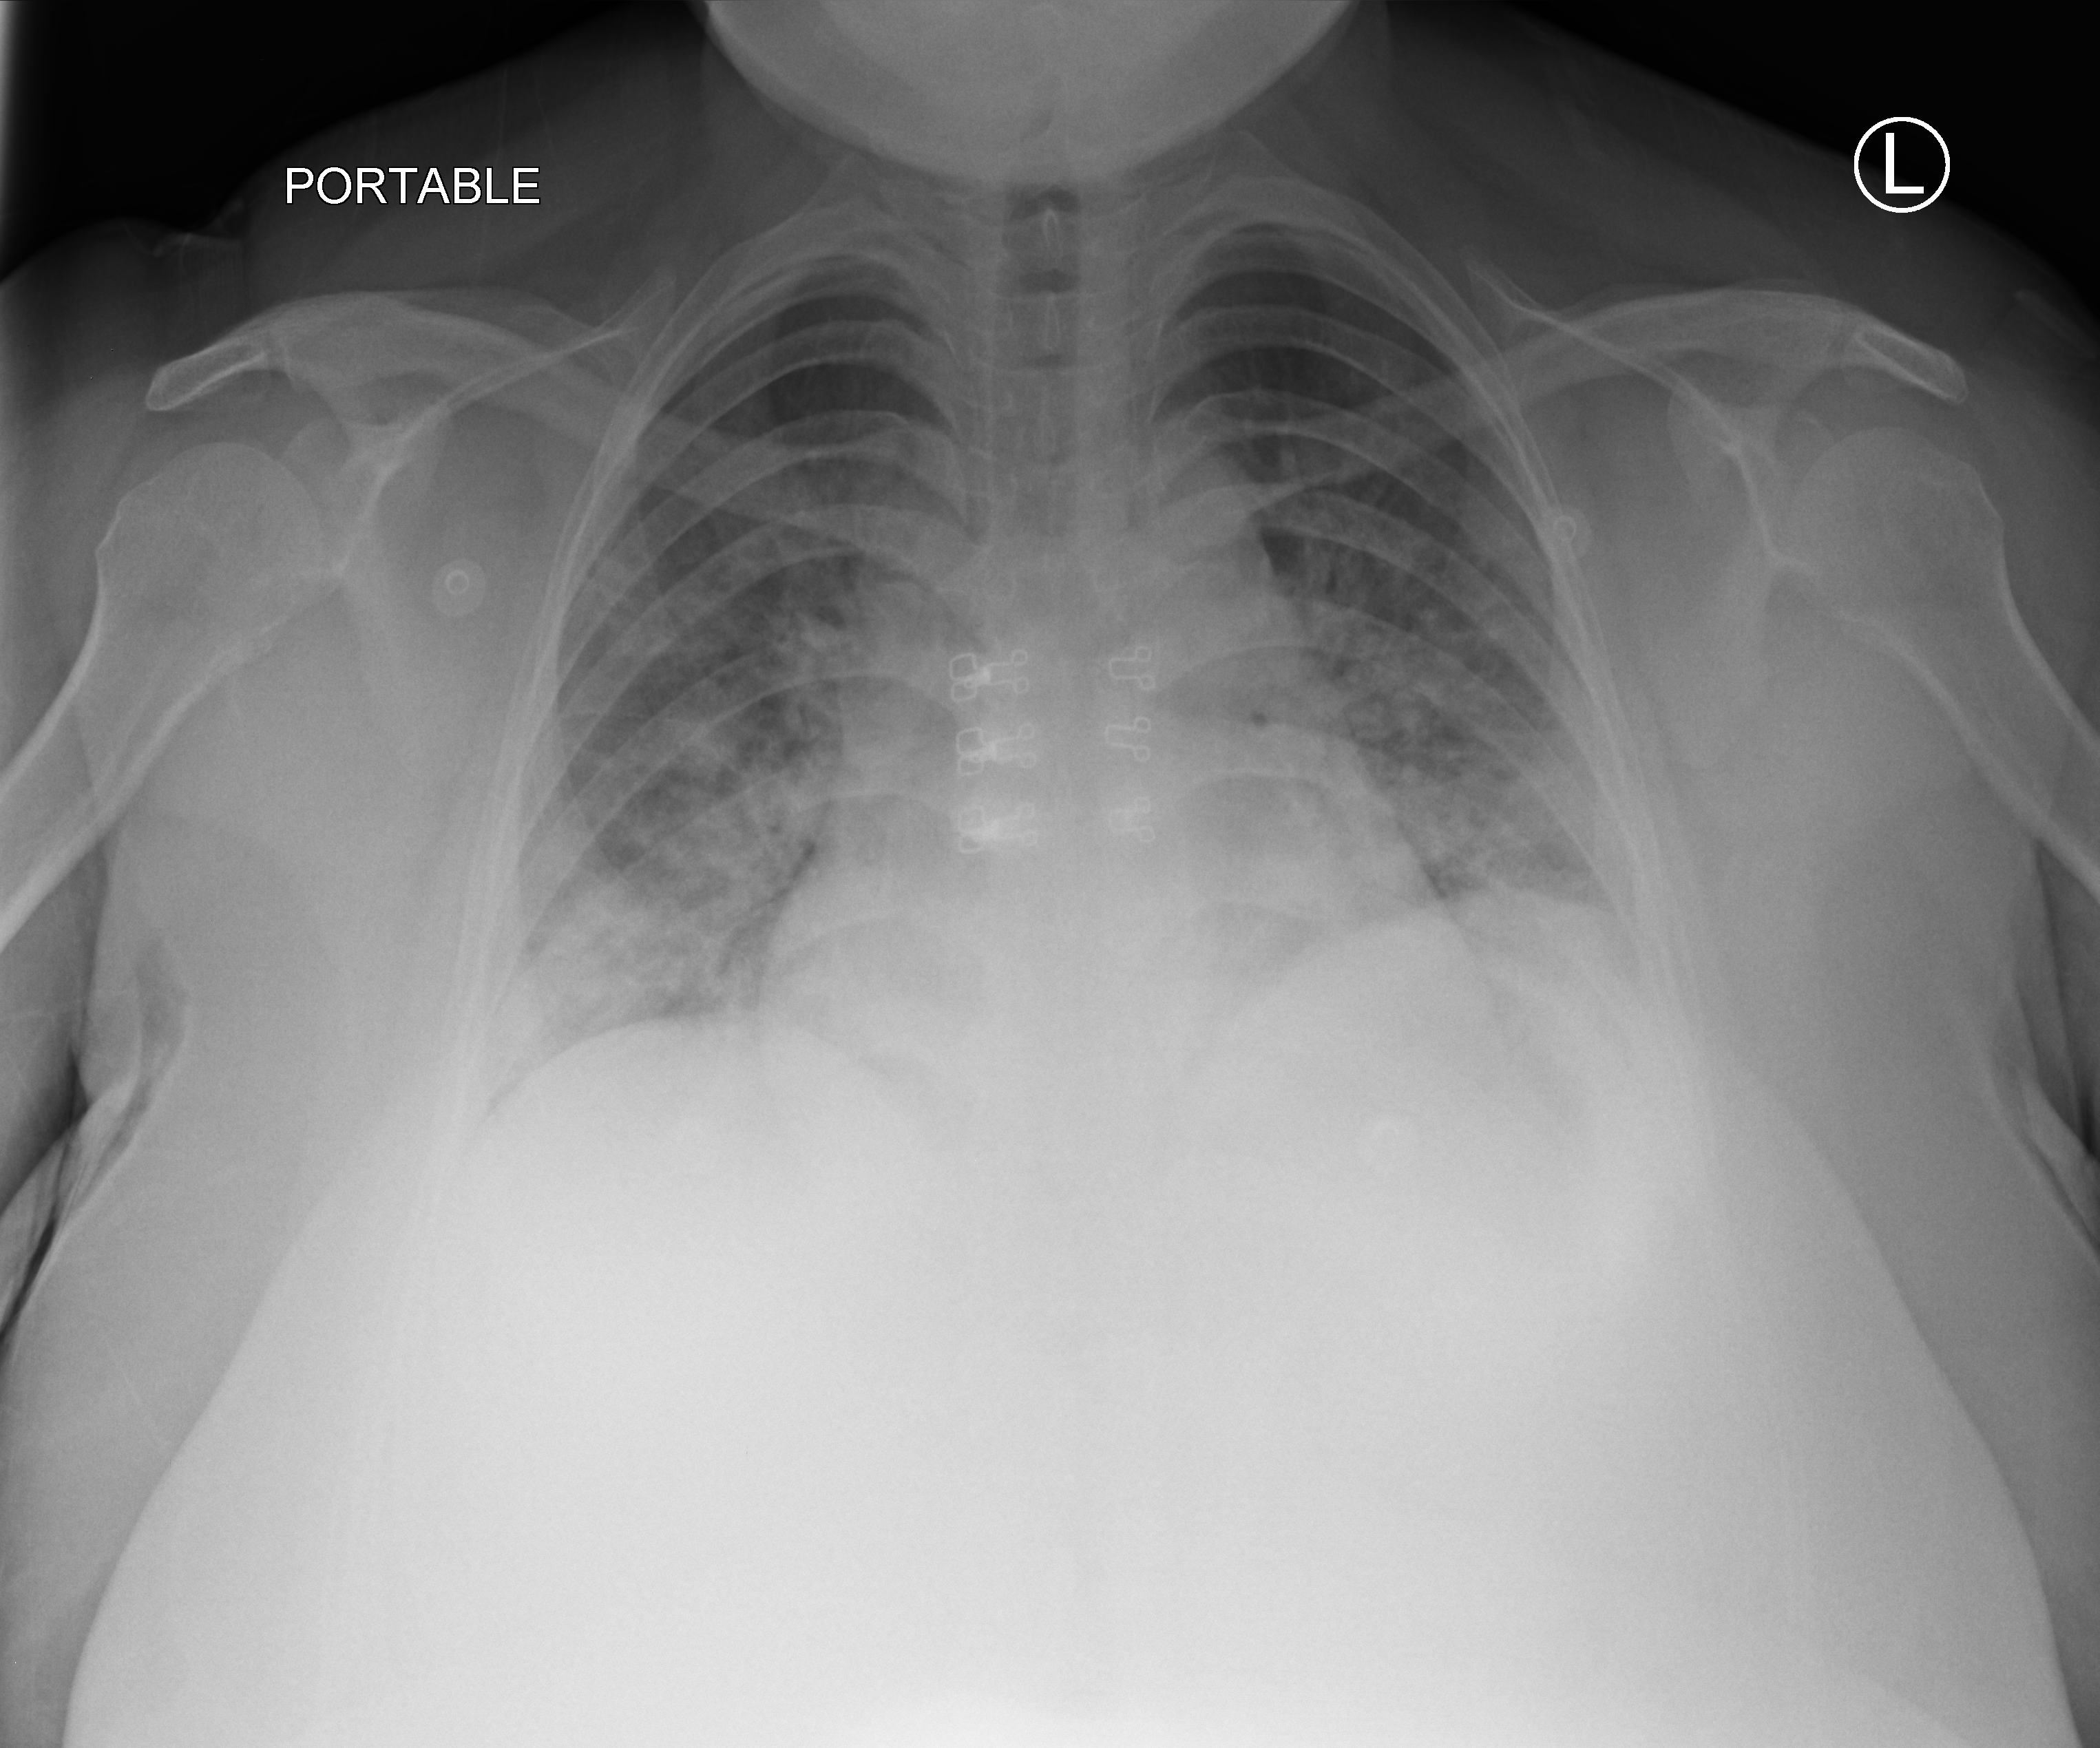
Bedside chest radiograph (computed radiography), anteroposterior (AP) projection. Female patient hospitalised with COVID-19, age 18–59 years.
Hospital-stay facts (about this admission, not read from this image; timing relative to this image not recorded): diabetes (admission record): no; admitted to intensive care during this hospital stay: no.